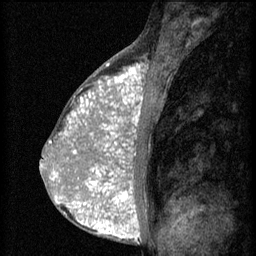
Breast MRI (dynamic contrast-enhanced), one sagittal slice. Position 36 of 60 along the scan axis. 3 images stored at this slice position (order not interpretable as contrast timing). 1.5 T. TE 4.2 ms, TR 8.2 ms. 256 × 256 image matrix, field of view 180 × 180 mm. Female patient, age 38 years.
Structures marked on this image (semi-automatically segmented with operator editing):
- analysis volume of interest (the breast-tissue region the enhancement analysis was run in; not a lesion): bounding box (x1, y1, x2, y2) in pixels: (92, 112, 151, 171)
- tumour enhancement mask (voxels above the 70 % enhancement threshold inside the analysis volume of interest): (92, 112, 140, 171)